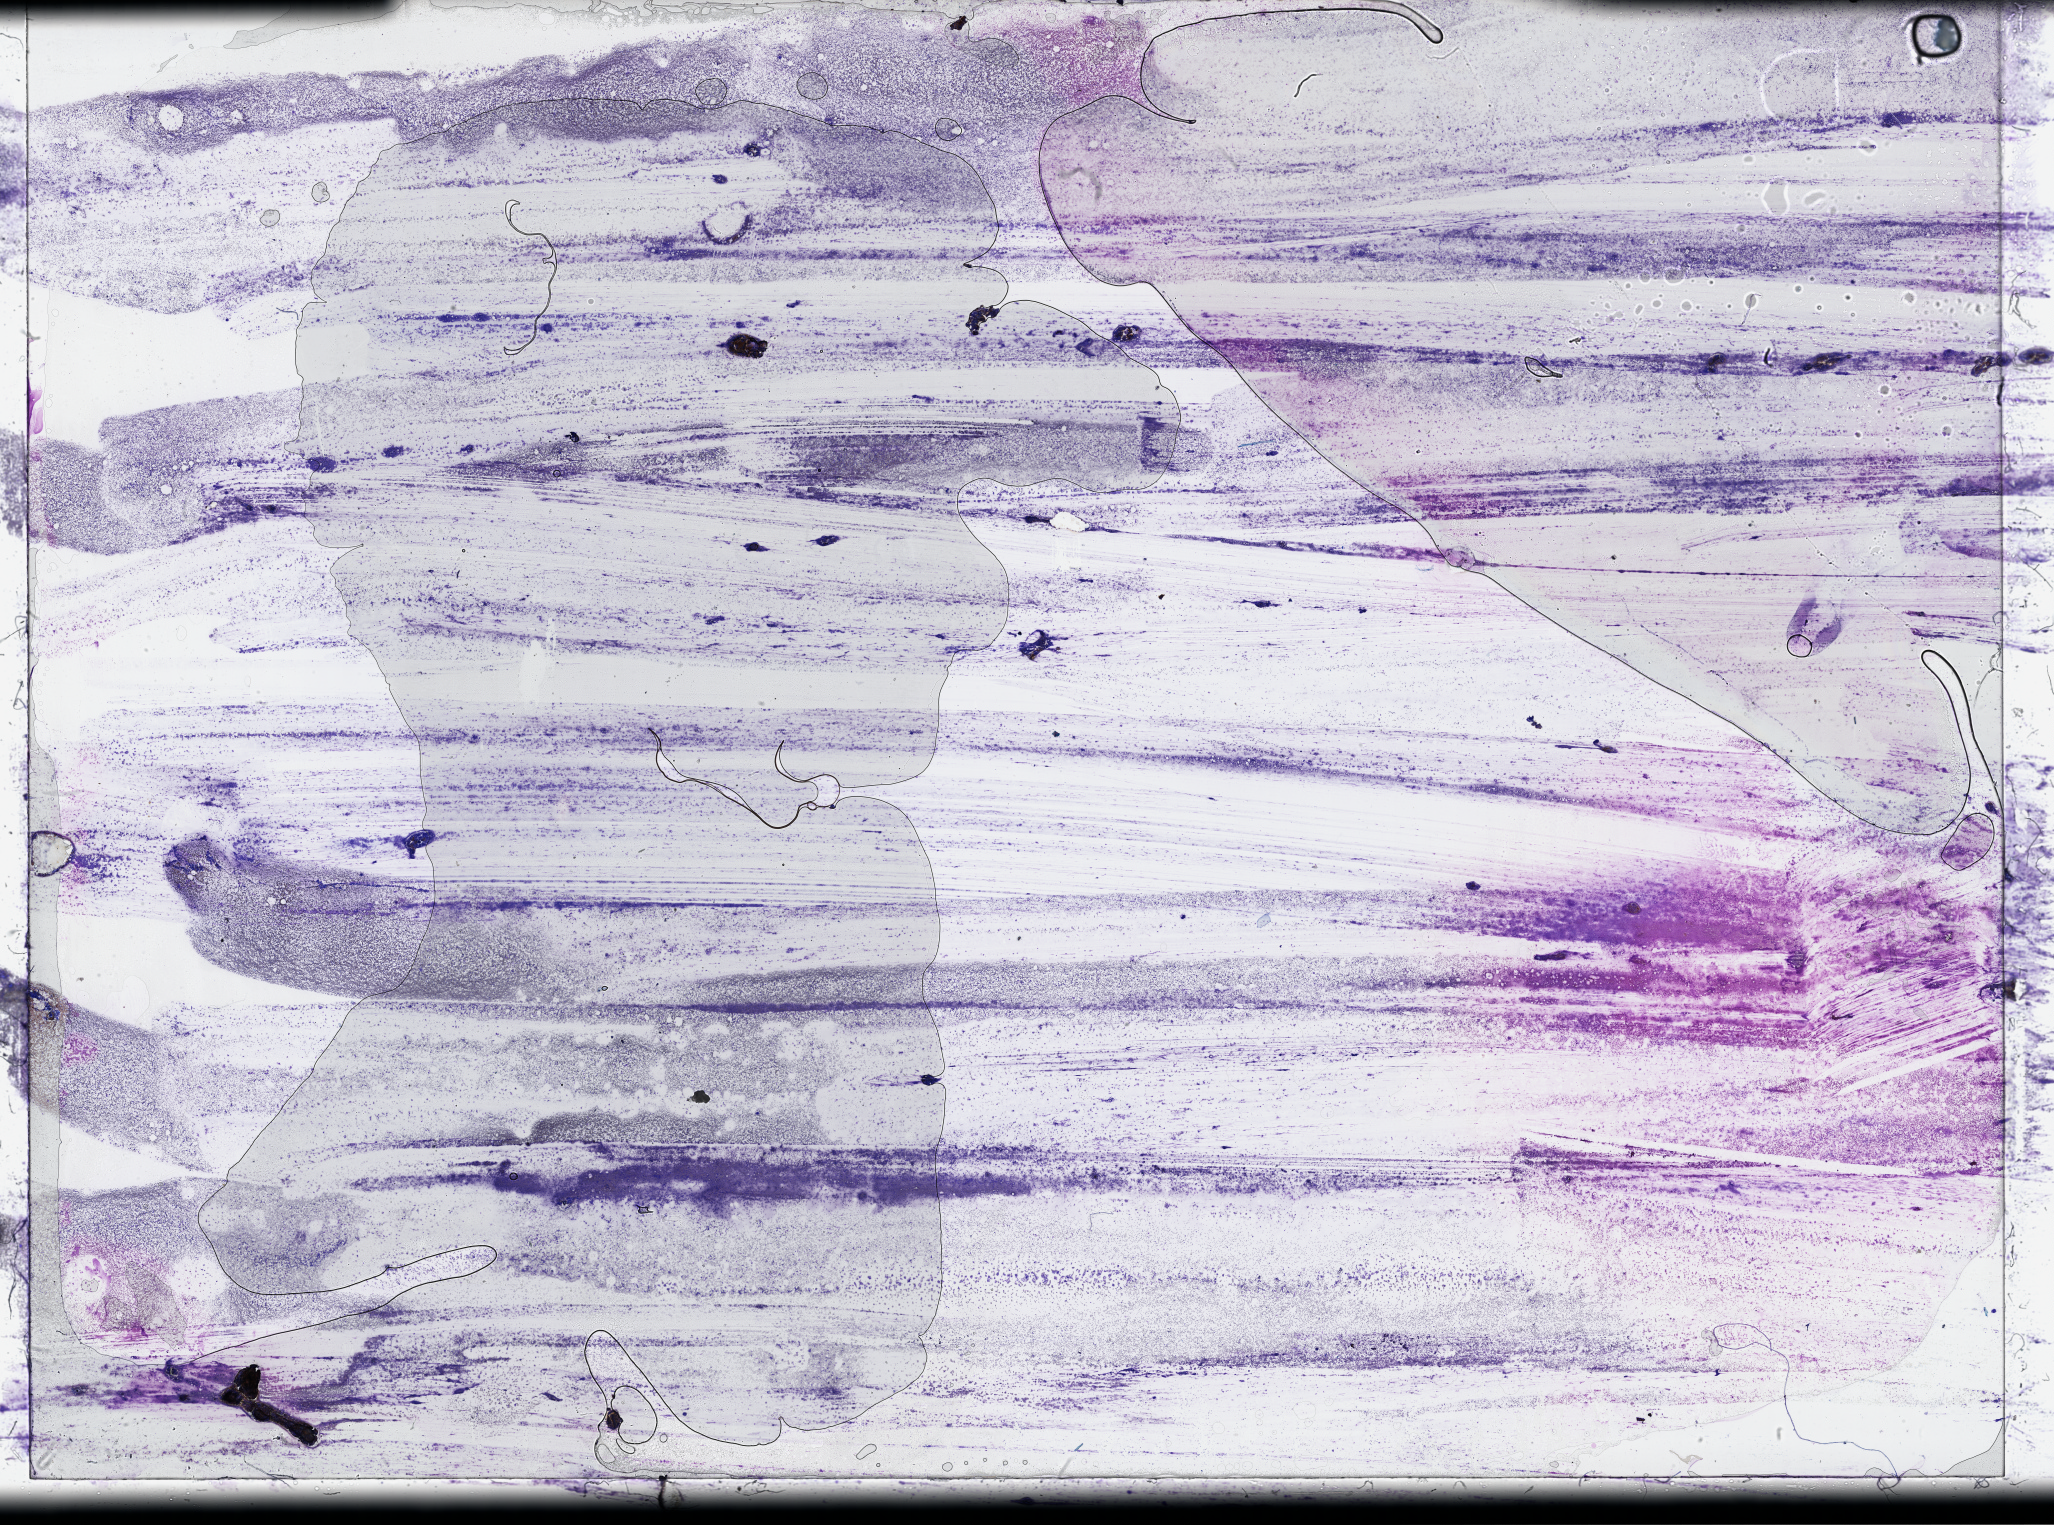
Whole-slide histology image, H&E — a low-resolution overview of the entire scanned area, about 33.2 x 24.6 mm (acquisition: 40x scan), bone marrow (leukaemic) sample. Male, 70 y/o.
Diagnosis: Acute Myeloid Leukemia.